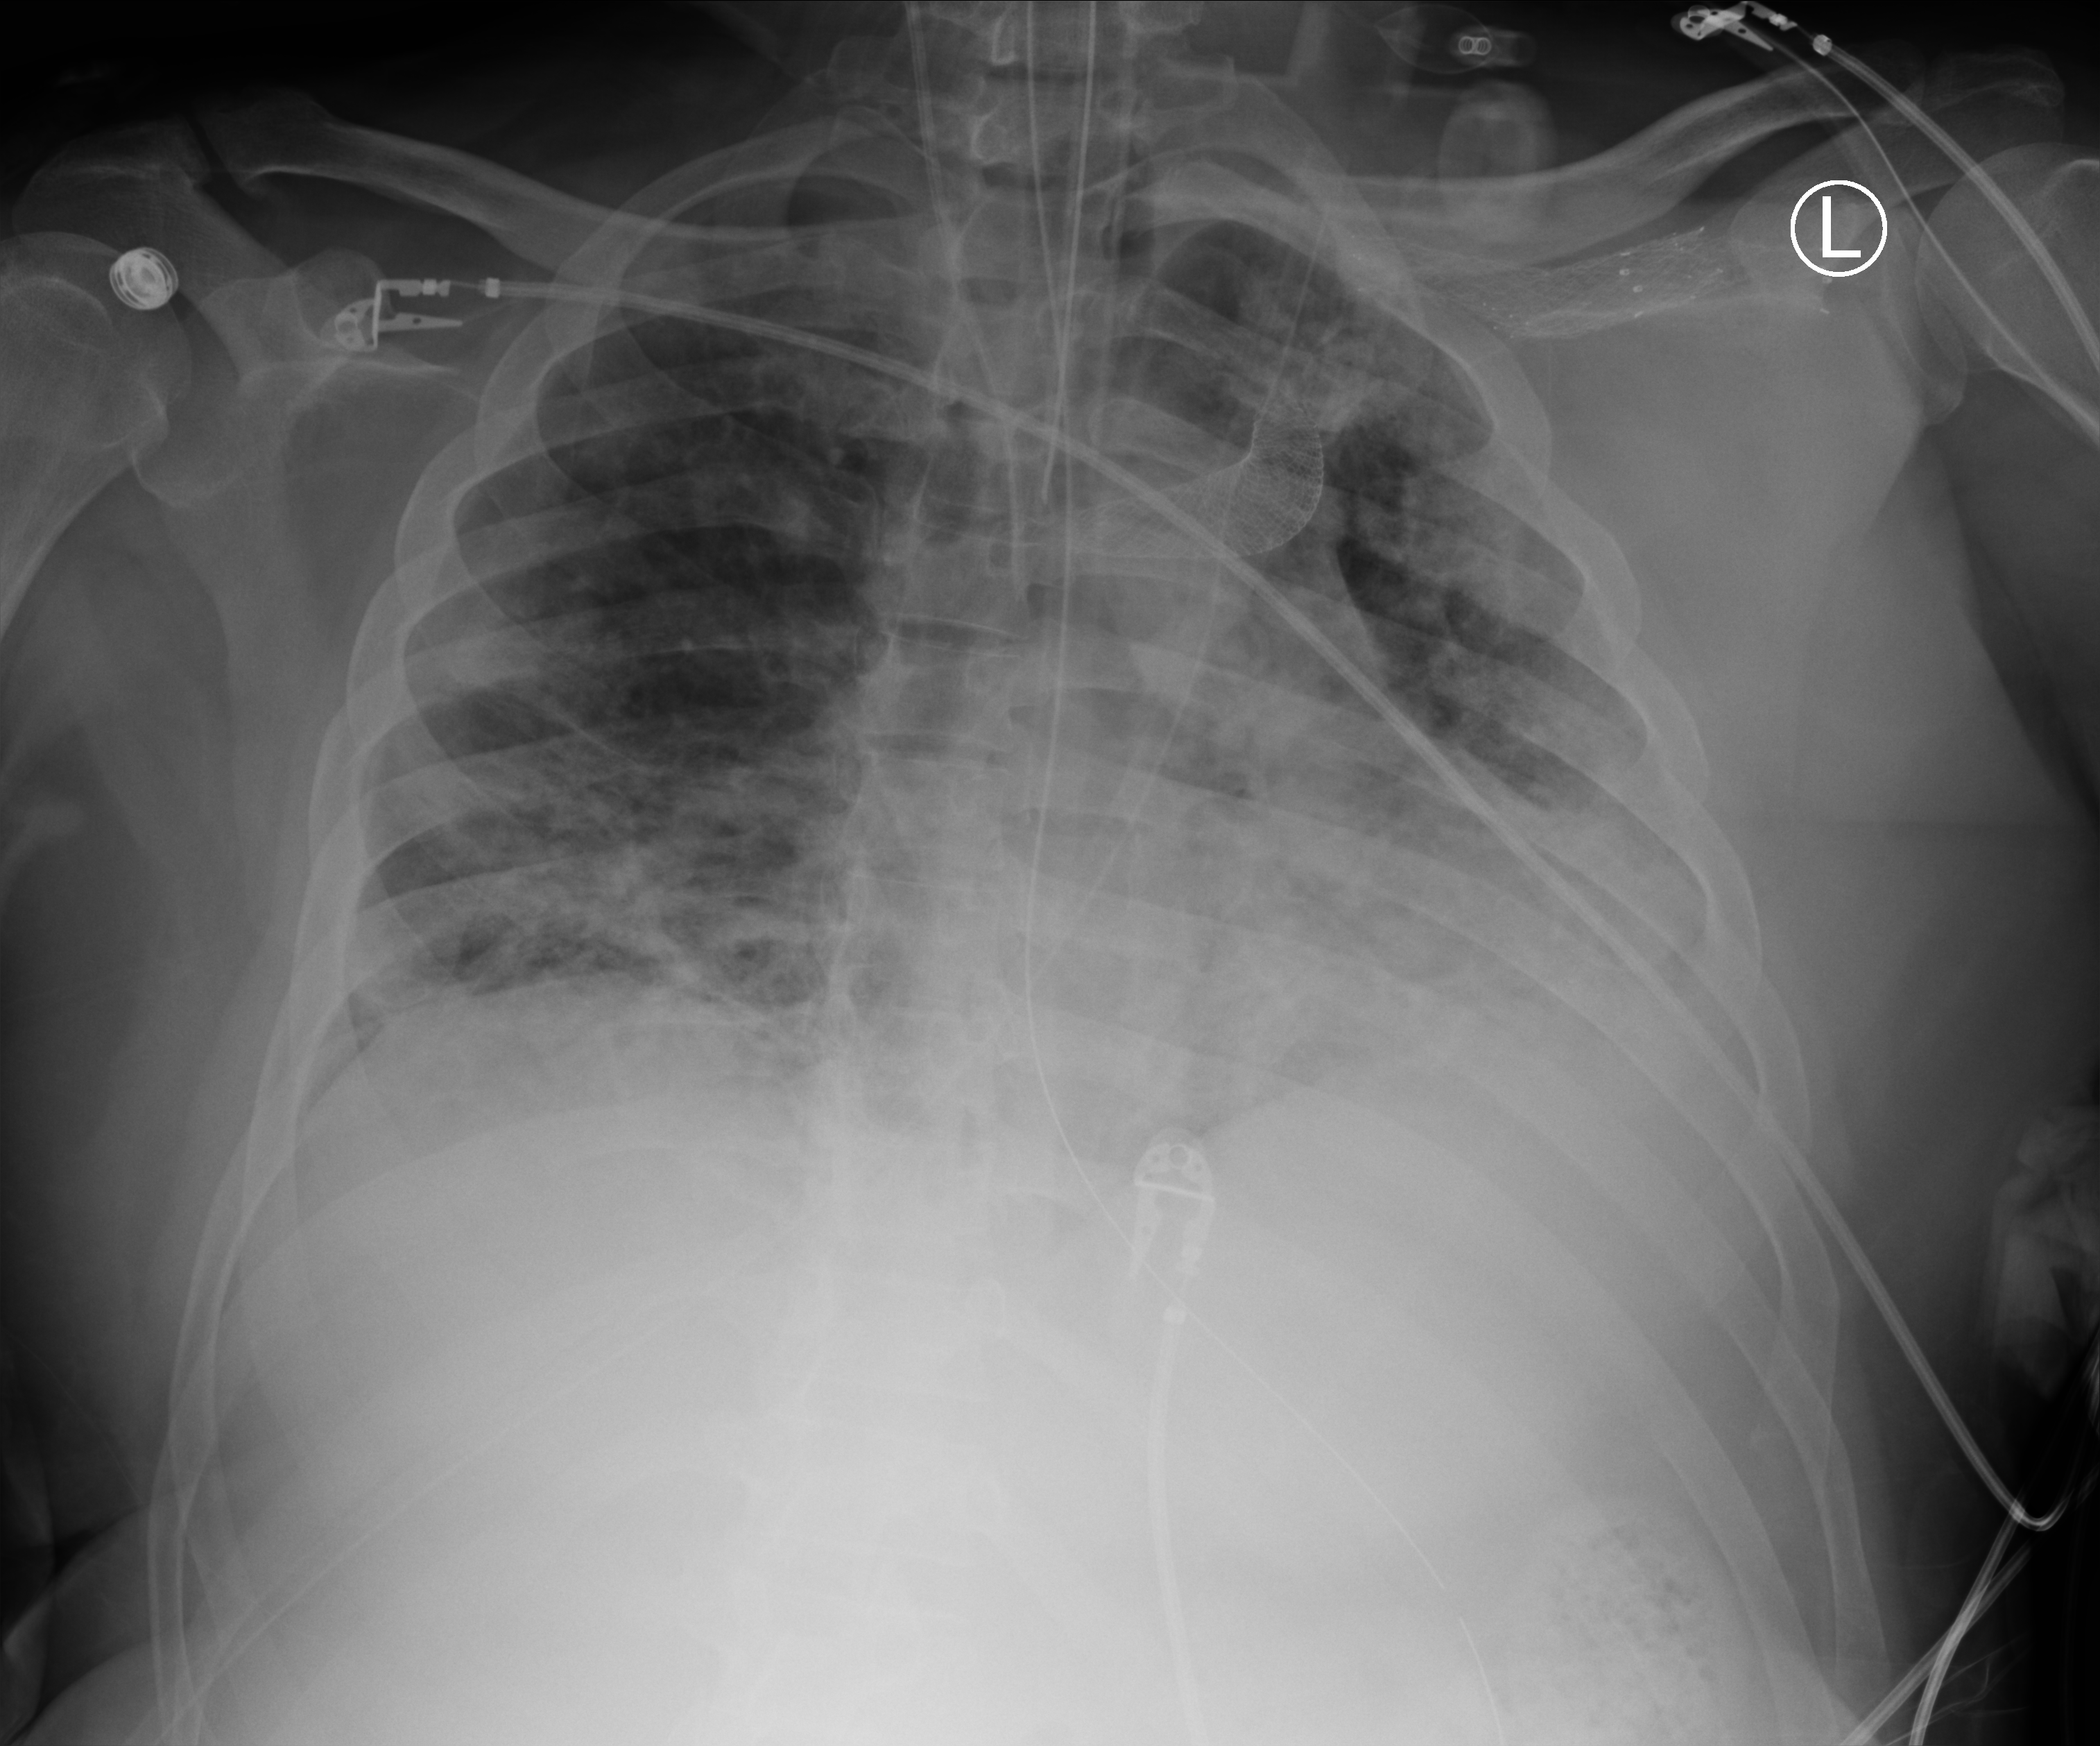
Bedside chest radiograph (computed radiography), anteroposterior (AP) projection. Patient hospitalised with COVID-19; male, aged 18–59 years.
Admission-level facts for this patient (not findings on this image; timing relative to this image not recorded): hypertension (admission record): yes; admitted to intensive care during this hospital stay: yes.